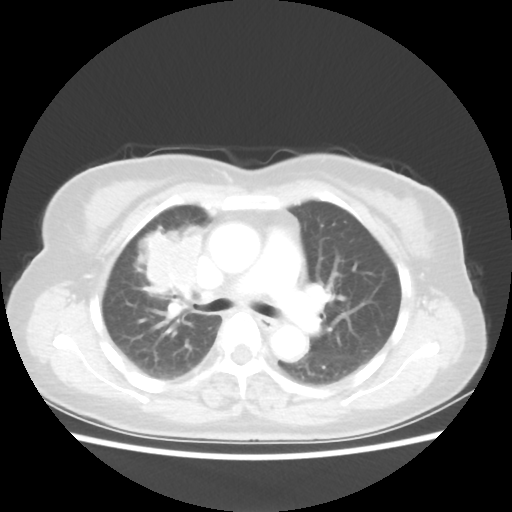
Chest CT, one axial slice; position 34 of 55 along the scan axis; reconstruction kernel STANDARD; lung window (W 1500 / L -600 HU); 5 mm slice thickness; 512 × 512 image matrix. Patient: female, 62 years. Case-level facts recorded for this patient, not image findings: clinical TNM (as recorded): T4 N3 M0.
Outlined on this slice (rectangle marked by the reading radiologist):
- lung tumour (recorded histology: squamous cell carcinoma): bounding box [x1, y1, x2, y2] px = [133, 215, 210, 308]